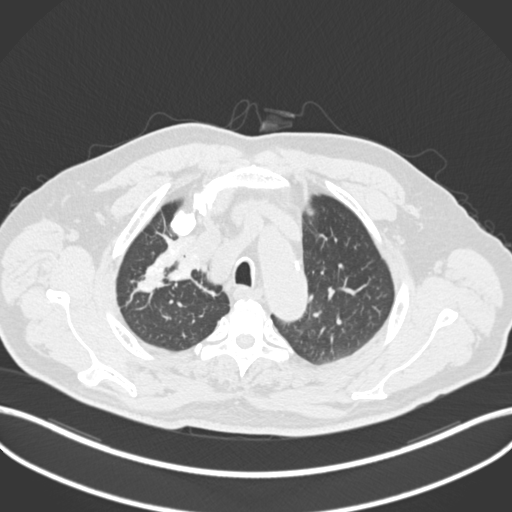
Chest CT, one axial slice; position 163 of 255 along the scan axis; 120 kVp; lung window (W 1500 / L -600 HU); 1 mm slice thickness; 512 × 512 image matrix, field of view 400 × 400 mm. Patient: male, 60 years. From the clinical record (not read from this slice): clinical TNM (as recorded): T1b N1 M0.
Structures marked on this image (rectangle marked by the reading radiologist):
- lung tumour (recorded histology: squamous cell carcinoma): bounding box (x1, y1, x2, y2) in pixels: (163, 246, 201, 296)